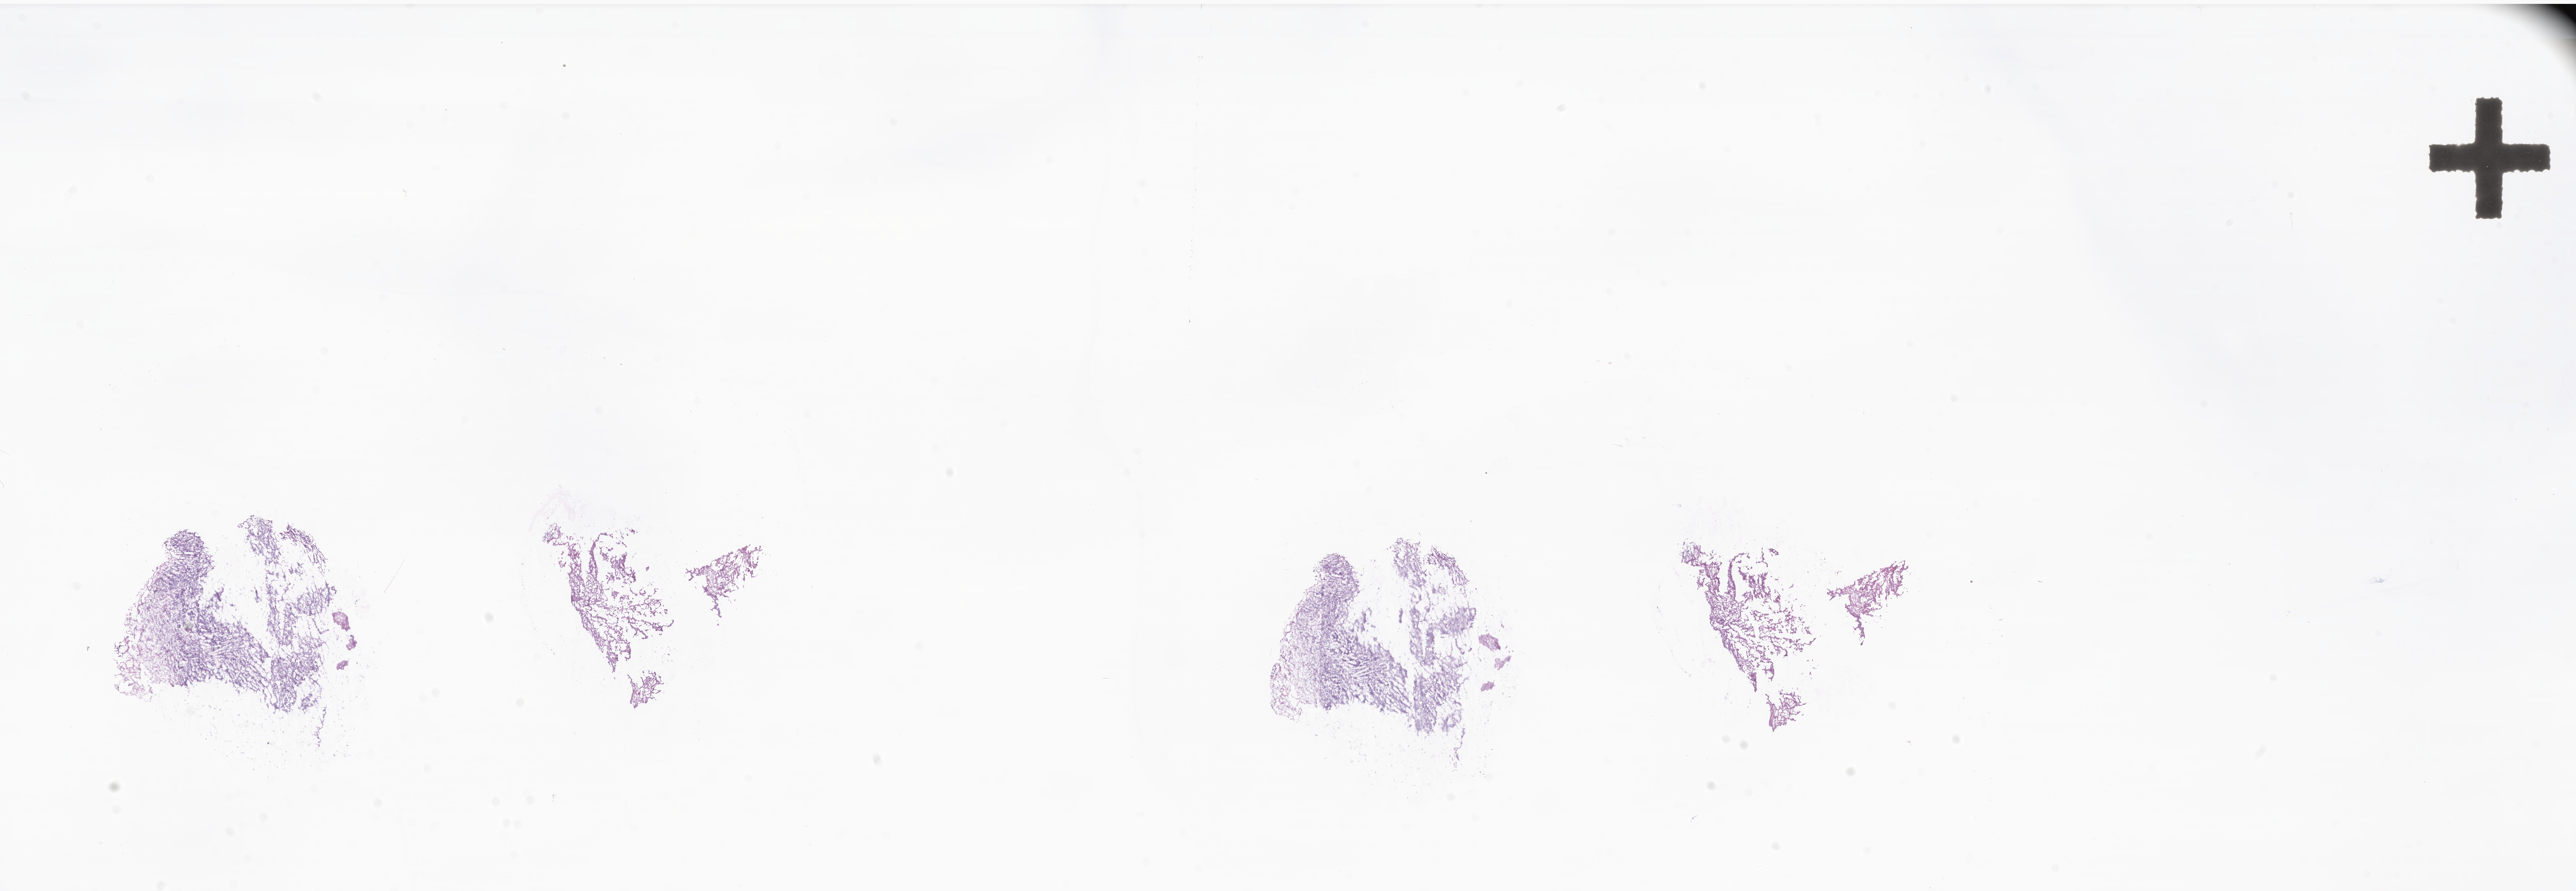
Haematoxylin and eosin whole-slide image — a low-resolution overview of the entire scanned area, about 41.8 x 14.4 mm, frozen section (tissue freezing medium), metastatic tumor tissue, resected from lymph node. Female patient; age at initial diagnosis 50 years. Slide review estimates, as recorded: tumor cells 80%, tumor nuclei 90%, stromal cells 10%, necrosis 10%, normal cells 0%. Inflammatory infiltration, as recorded: lymphocyte infiltration 0%, monocyte infiltration 0%, neutrophil infiltration 0%.
Patient diagnosis (primary): Malignant melanoma, NOS. Section: bottom of the tissue portion.